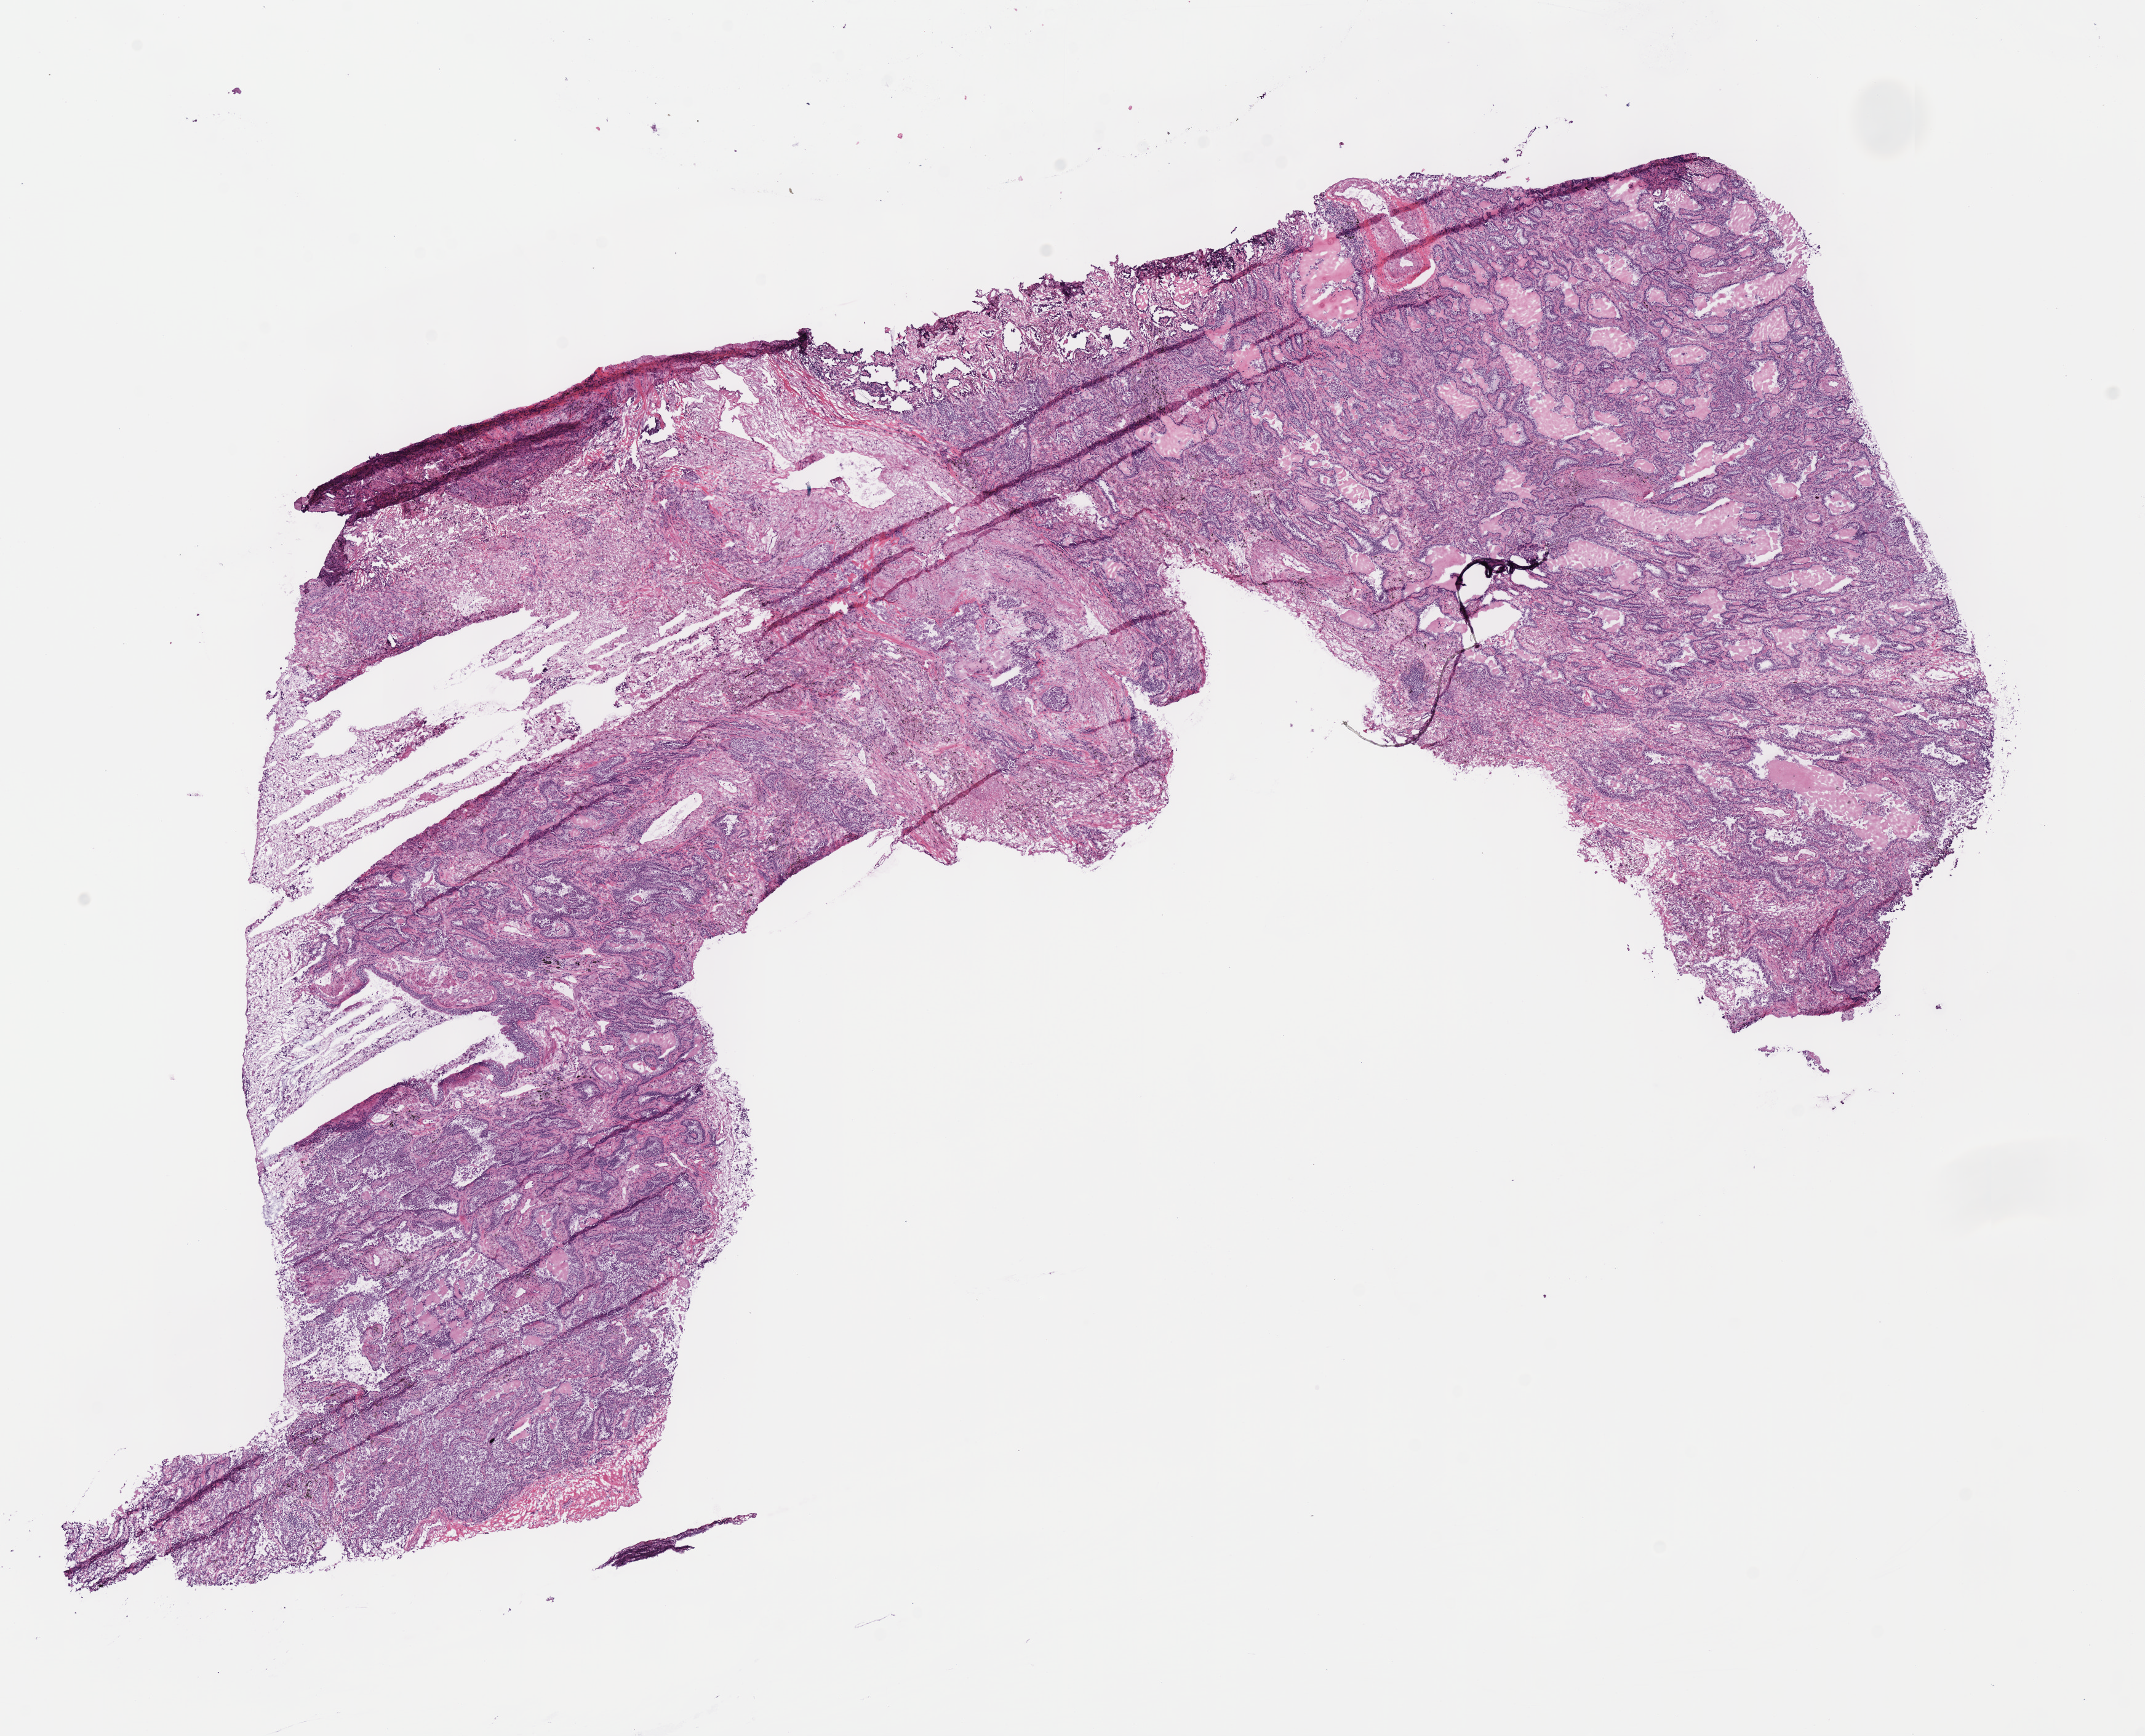
H&E-stained whole-slide image — low-resolution overview of the scanned area, about 13.7 x 11.1 mm (acquisition: 40x scan); frozen section from the top of the tissue portion; primary tumour sample from the lung. Male, age 70 years at initial diagnosis.
Diagnosis: Adenocarcinoma, NOS (upper lobe, lung).